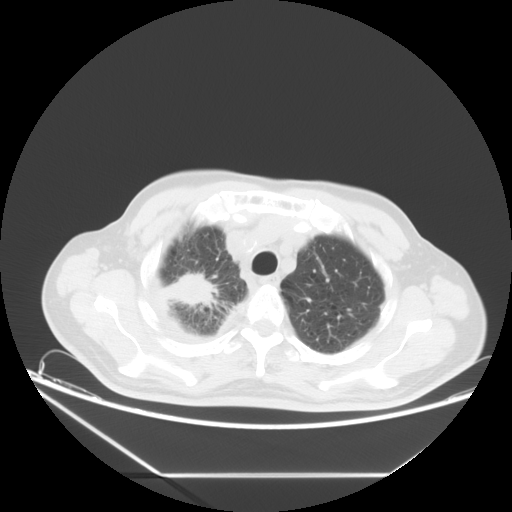
Chest CT, one axial slice. Reconstruction kernel STANDARD. Lung window (W 1500 / L -600 HU). 5 mm slice thickness. 512 × 512 image matrix, field of view 418 × 418 mm. Patient: male, 75 years. Case-level facts recorded for this patient, not image findings: clinical TNM (as recorded): T1c N1 M1.
Annotated regions visible in this slice (bounding box drawn by a radiologist):
- lung tumour (recorded histology: adenocarcinoma): bounding box (x1, y1, x2, y2) in pixels: (157, 272, 218, 313)